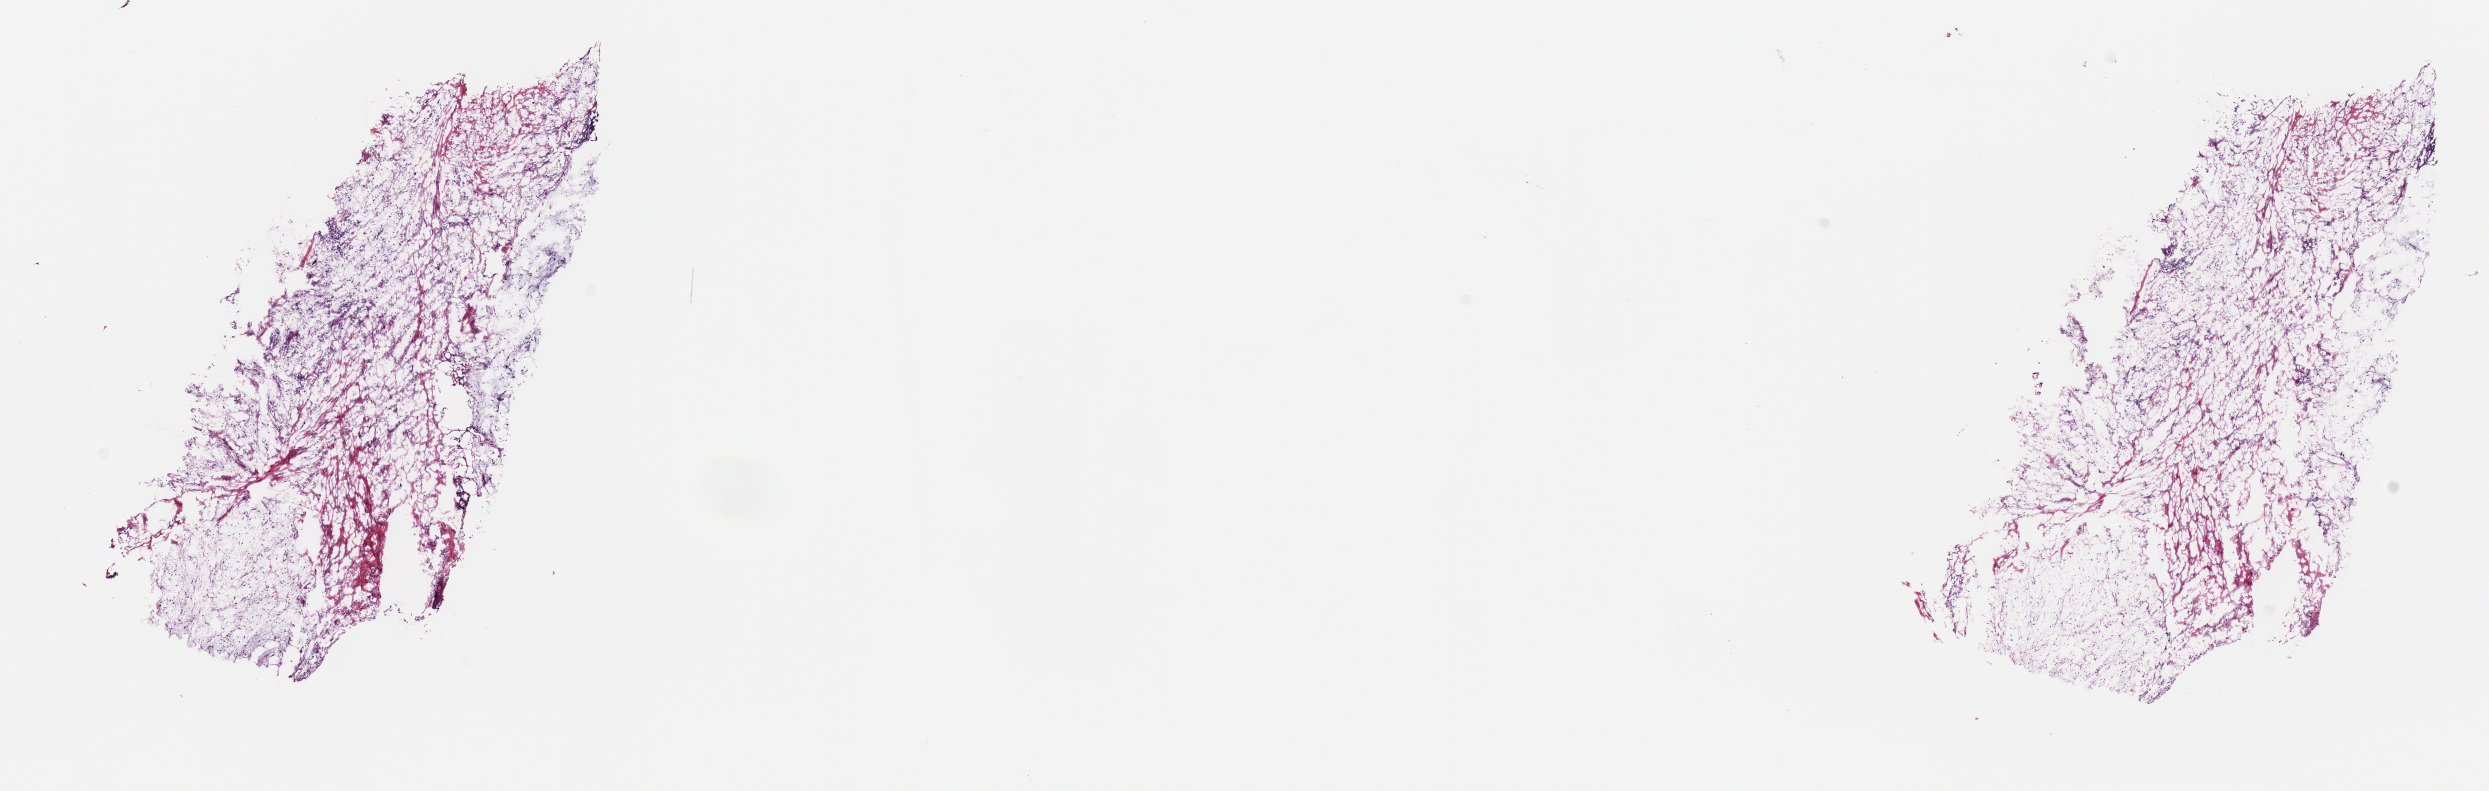
Whole-slide histology image, H&E, a low-resolution overview of the entire scanned area, about 20.1 x 6.4 mm; frozen section from the top of the tissue portion; primary tumour sample from the retroperitoneum and peritoneum. Female, age 50 years at initial diagnosis. Slide review estimates, as recorded: tumour cells 100%, tumour nuclei 80%, normal cells 0%, stromal cells 0%, necrosis 0%. Inflammatory infiltration, as recorded: lymphocyte infiltration 0%, monocyte infiltration 0%, neutrophil infiltration 0%.
Diagnosis: Dedifferentiated liposarcoma (retroperitoneum).